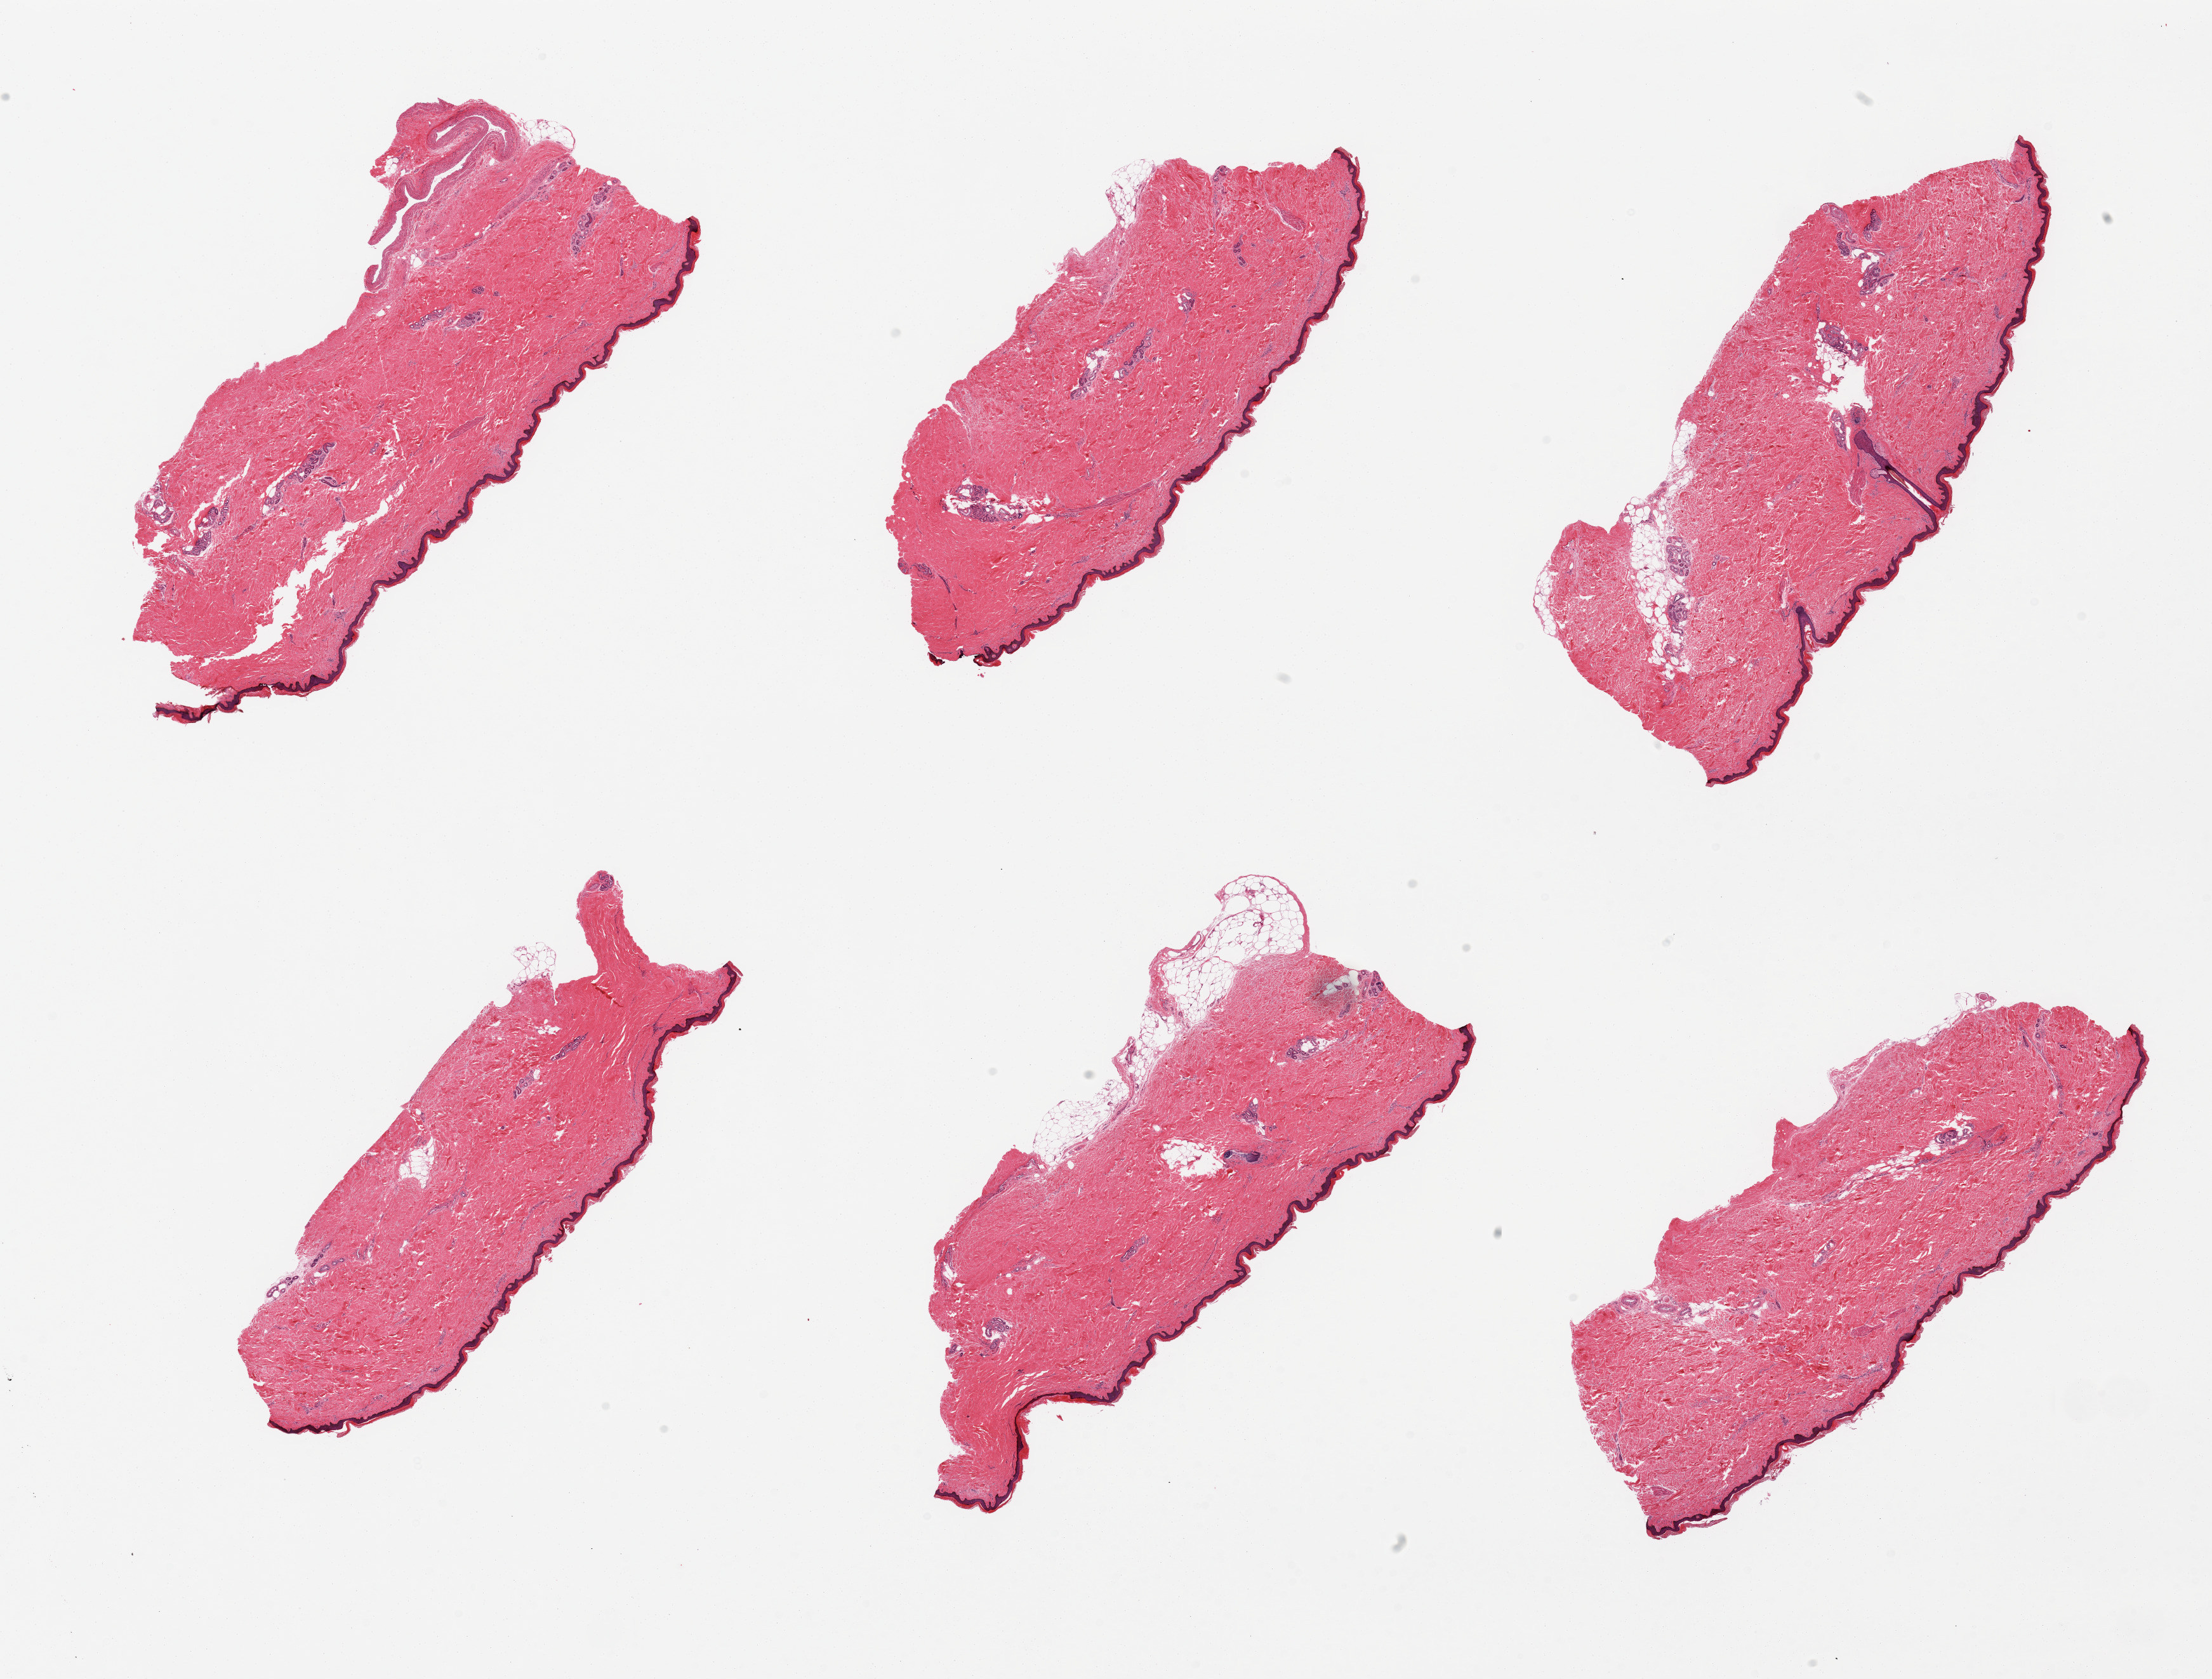
Digitized H&E-stained section, a low-resolution overview of the entire scanned area, about 27.6 x 20.9 mm (from a 20x scan). PAXgene-fixed paraffin-embedded (PFPE) section. Sampled site (target tissue): skin of lower leg. Tissue donor sample. Male donor.
Reviewer comment on this tissue sample: 6 pieces, squamous epithelium is ~50 micrrons, trace adherent dermal fat, ~1mm.